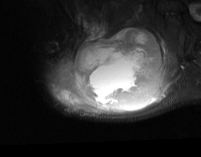
MRI of an extremity soft-tissue mass, one axial slice. Position 50 of 74 along the scan axis. STIR. MR volume resampled by the dataset authors to the PET/CT grid (not the native acquisition matrix). 201 × 157 image matrix. Male patient. From the clinical record (not read from this slice): histological type: pleiomorphic spindle cell undifferentiated; grade: high; site of the primary tumour: right parascapusular.
Structures marked on this image (expert contour drawn on MRI and transferred to this co-registered scan by the dataset authors):
- gross tumour volume including surrounding oedema: bounding box <47,22,178,115> (left, top, right, bottom; pixels)
- gross tumour volume (mass): <74,29,162,110>